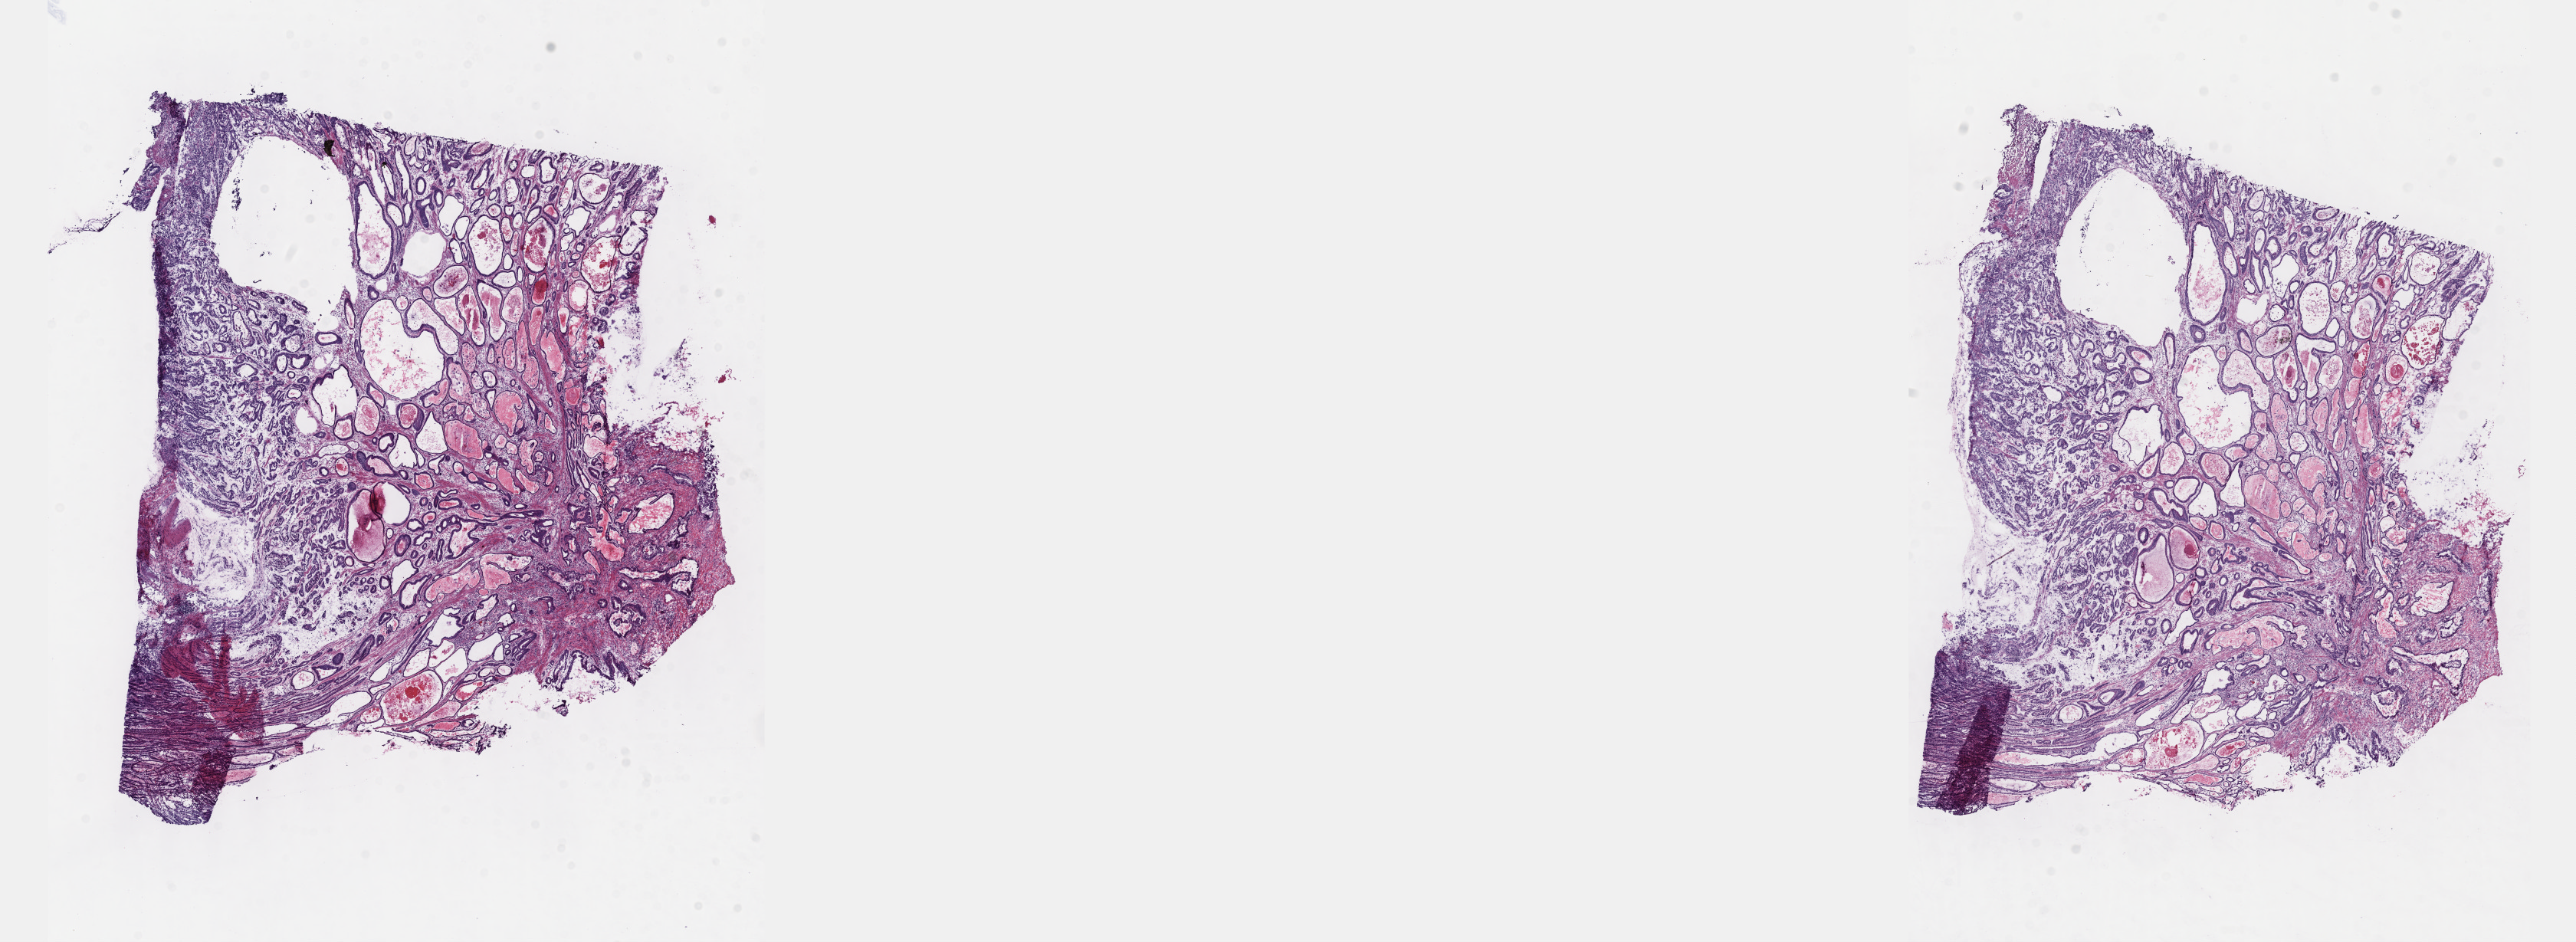
Digitized H&E-stained tissue section (whole slide), a low-resolution overview of the entire scanned area, about 27.2 x 9.9 mm (acquisition: 40x scan); frozen section from the top of the tissue portion; esophagus, primary tumour sample. Patient: male, age at initial diagnosis 57 years. Histologic grade: GX (grade cannot be assessed). Pathologist review of this section (percent, as recorded): tumour cells 60%, tumour nuclei 96%, normal cells 0%, stromal cells 40%, necrosis 0%. Inflammatory infiltration, as recorded: lymphocyte infiltration 2%, monocyte infiltration 6%, neutrophil infiltration 0%.
AJCC pathologic stage: IVA. TNM: T1 N0 M1a. Pathologic diagnosis: Adenocarcinoma, NOS.